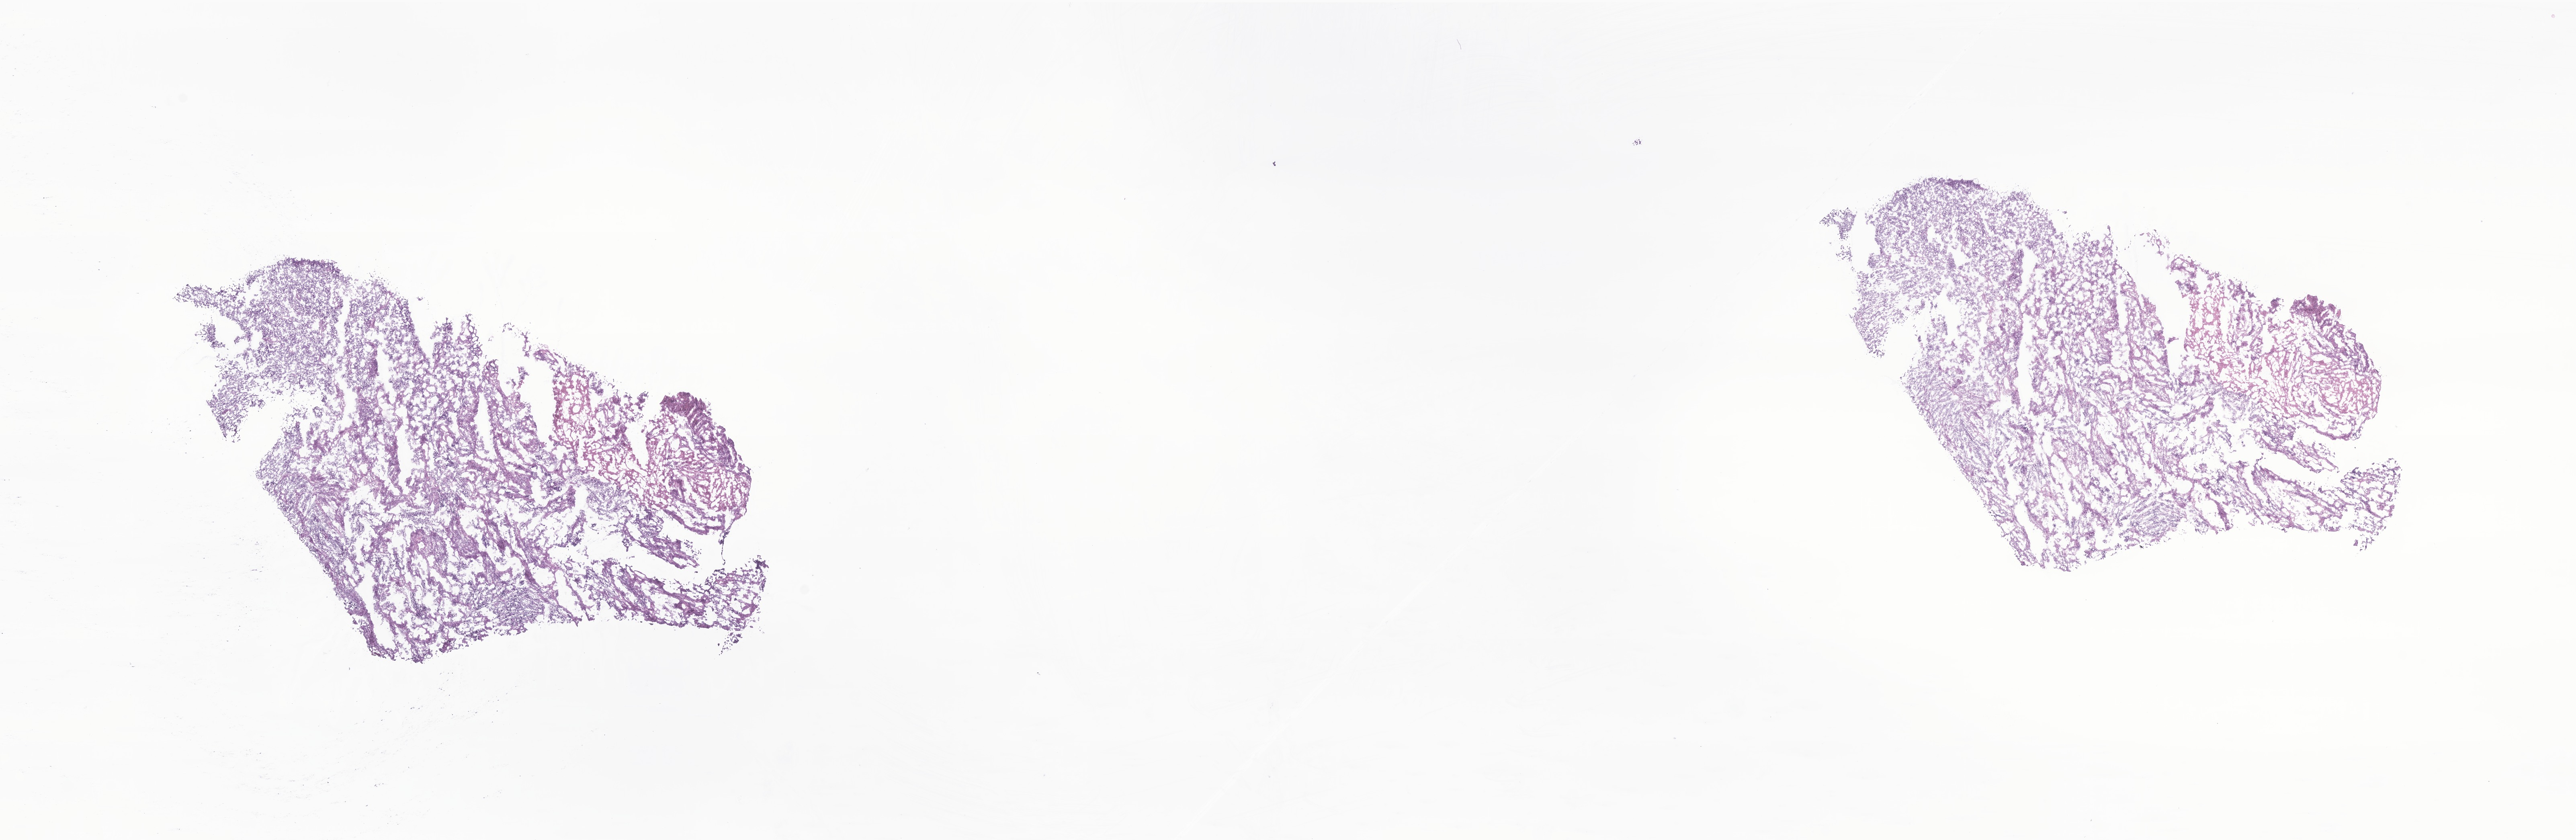
Whole-slide image, hematoxylin and eosin (H&E) stain of tumor tissue from the adrenal gland — low-resolution overview of the scanned area, about 27.0 x 8.8 mm; cryosection (OCT / tissue freezing medium). Patient male; age 80 months (6 years 8 months).
* recorded diagnosis: Neuroblastoma, NOS